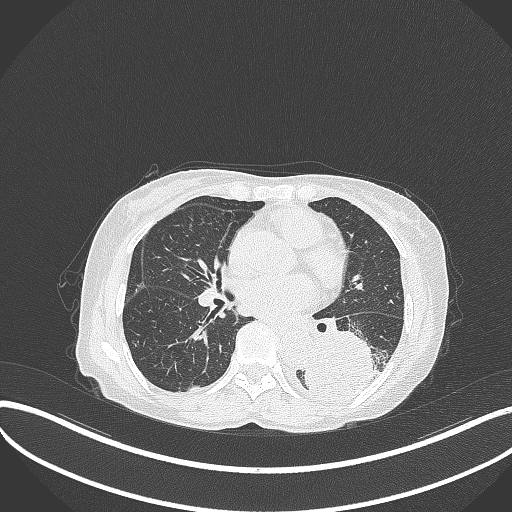
Chest CT, one axial slice. Slice 147 of 370 in the series (ordered by position). Reconstruction kernel B70f. 120 kVp. Lung window (W 1500 / L -600 HU). 1 mm slice thickness. 512 × 512 image matrix, field of view 400 × 400 mm. Female patient, age 78 years. Case-level facts recorded for this patient, not image findings: clinical TNM (as recorded): T3 N0 M1.
Annotated regions visible in this slice (bounding box drawn by a radiologist):
- lung tumour (recorded histology: squamous cell carcinoma): box from (x=299, y=332) to (x=383, y=404) px